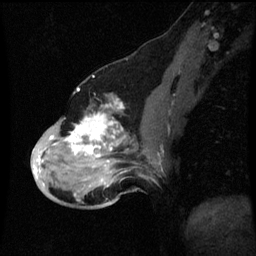
Breast MRI (dynamic contrast-enhanced), one sagittal slice. Slice 28 of 60 in the series (ordered by position). Dynamic contrast-enhanced series, image 2 of 3 at this slice position (ordered by acquisition). 1.5 T. TE 4.2 ms, TR 8.9 ms. 2 mm slice thickness. 256 × 256 image matrix, field of view 200 × 200 mm. Patient: female, 49 years. Case-level facts recorded for this patient, not image findings: setting: breast cancer imaged before/during neoadjuvant chemotherapy; receptor status: HR-positive, HER2-negative.
Annotated regions visible in this slice (semi-automatically segmented with operator editing):
- analysis volume of interest (the breast-tissue region the enhancement analysis was run in; not a lesion): bounding box <32,100,159,199> (left, top, right, bottom; pixels)
- tumour enhancement mask (voxels above the 70 % enhancement threshold inside the analysis volume of interest): <34,102,127,187>